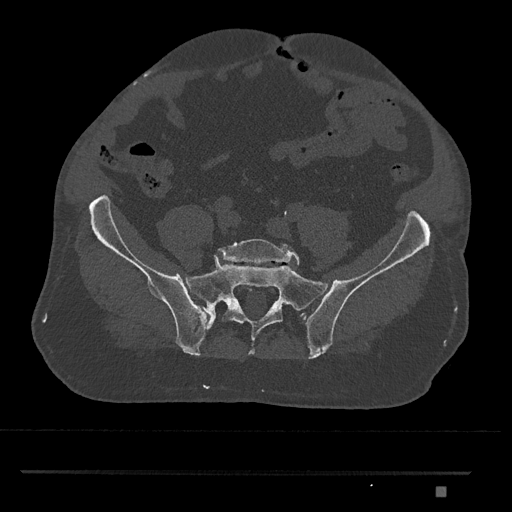
CT including the spine, one axial slice. Position 511 of 1134 along the scan axis. Reconstruction kernel Br40s/3. 120 kVp. Bone window (W 1800 / L 400 HU). 0.5 mm slice thickness. 512 × 512 image matrix. Male patient, age 65 years. Case-level facts recorded for this patient, not image findings: primary cancer: prostate.
Annotated regions visible in this slice (semi-automatically segmented with operator editing):
- L5 vertebra: bounding box (x1, y1, x2, y2) in pixels: (217, 239, 300, 265)